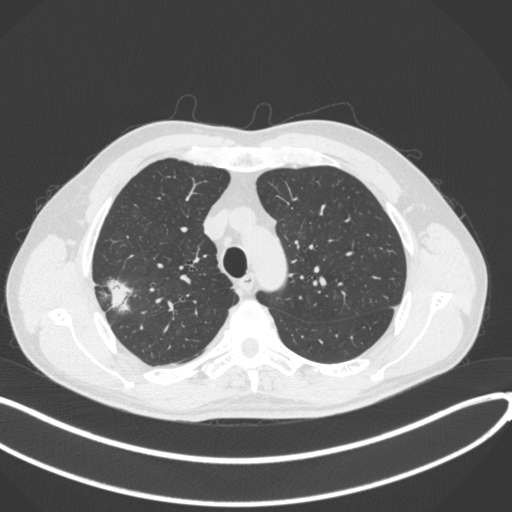
Chest CT, one axial slice. Position 317 of 381 along the scan axis. 120 kVp. Lung window (W 1500 / L -600 HU). 512 × 512 image matrix. Patient: male, 62 years. From the clinical record (not read from this slice): clinical TNM (as recorded): T1c N0 M0.
Structures marked on this image (rectangle marked by the reading radiologist):
- lung tumour (recorded histology: adenocarcinoma): box from (x=97, y=271) to (x=133, y=314) px